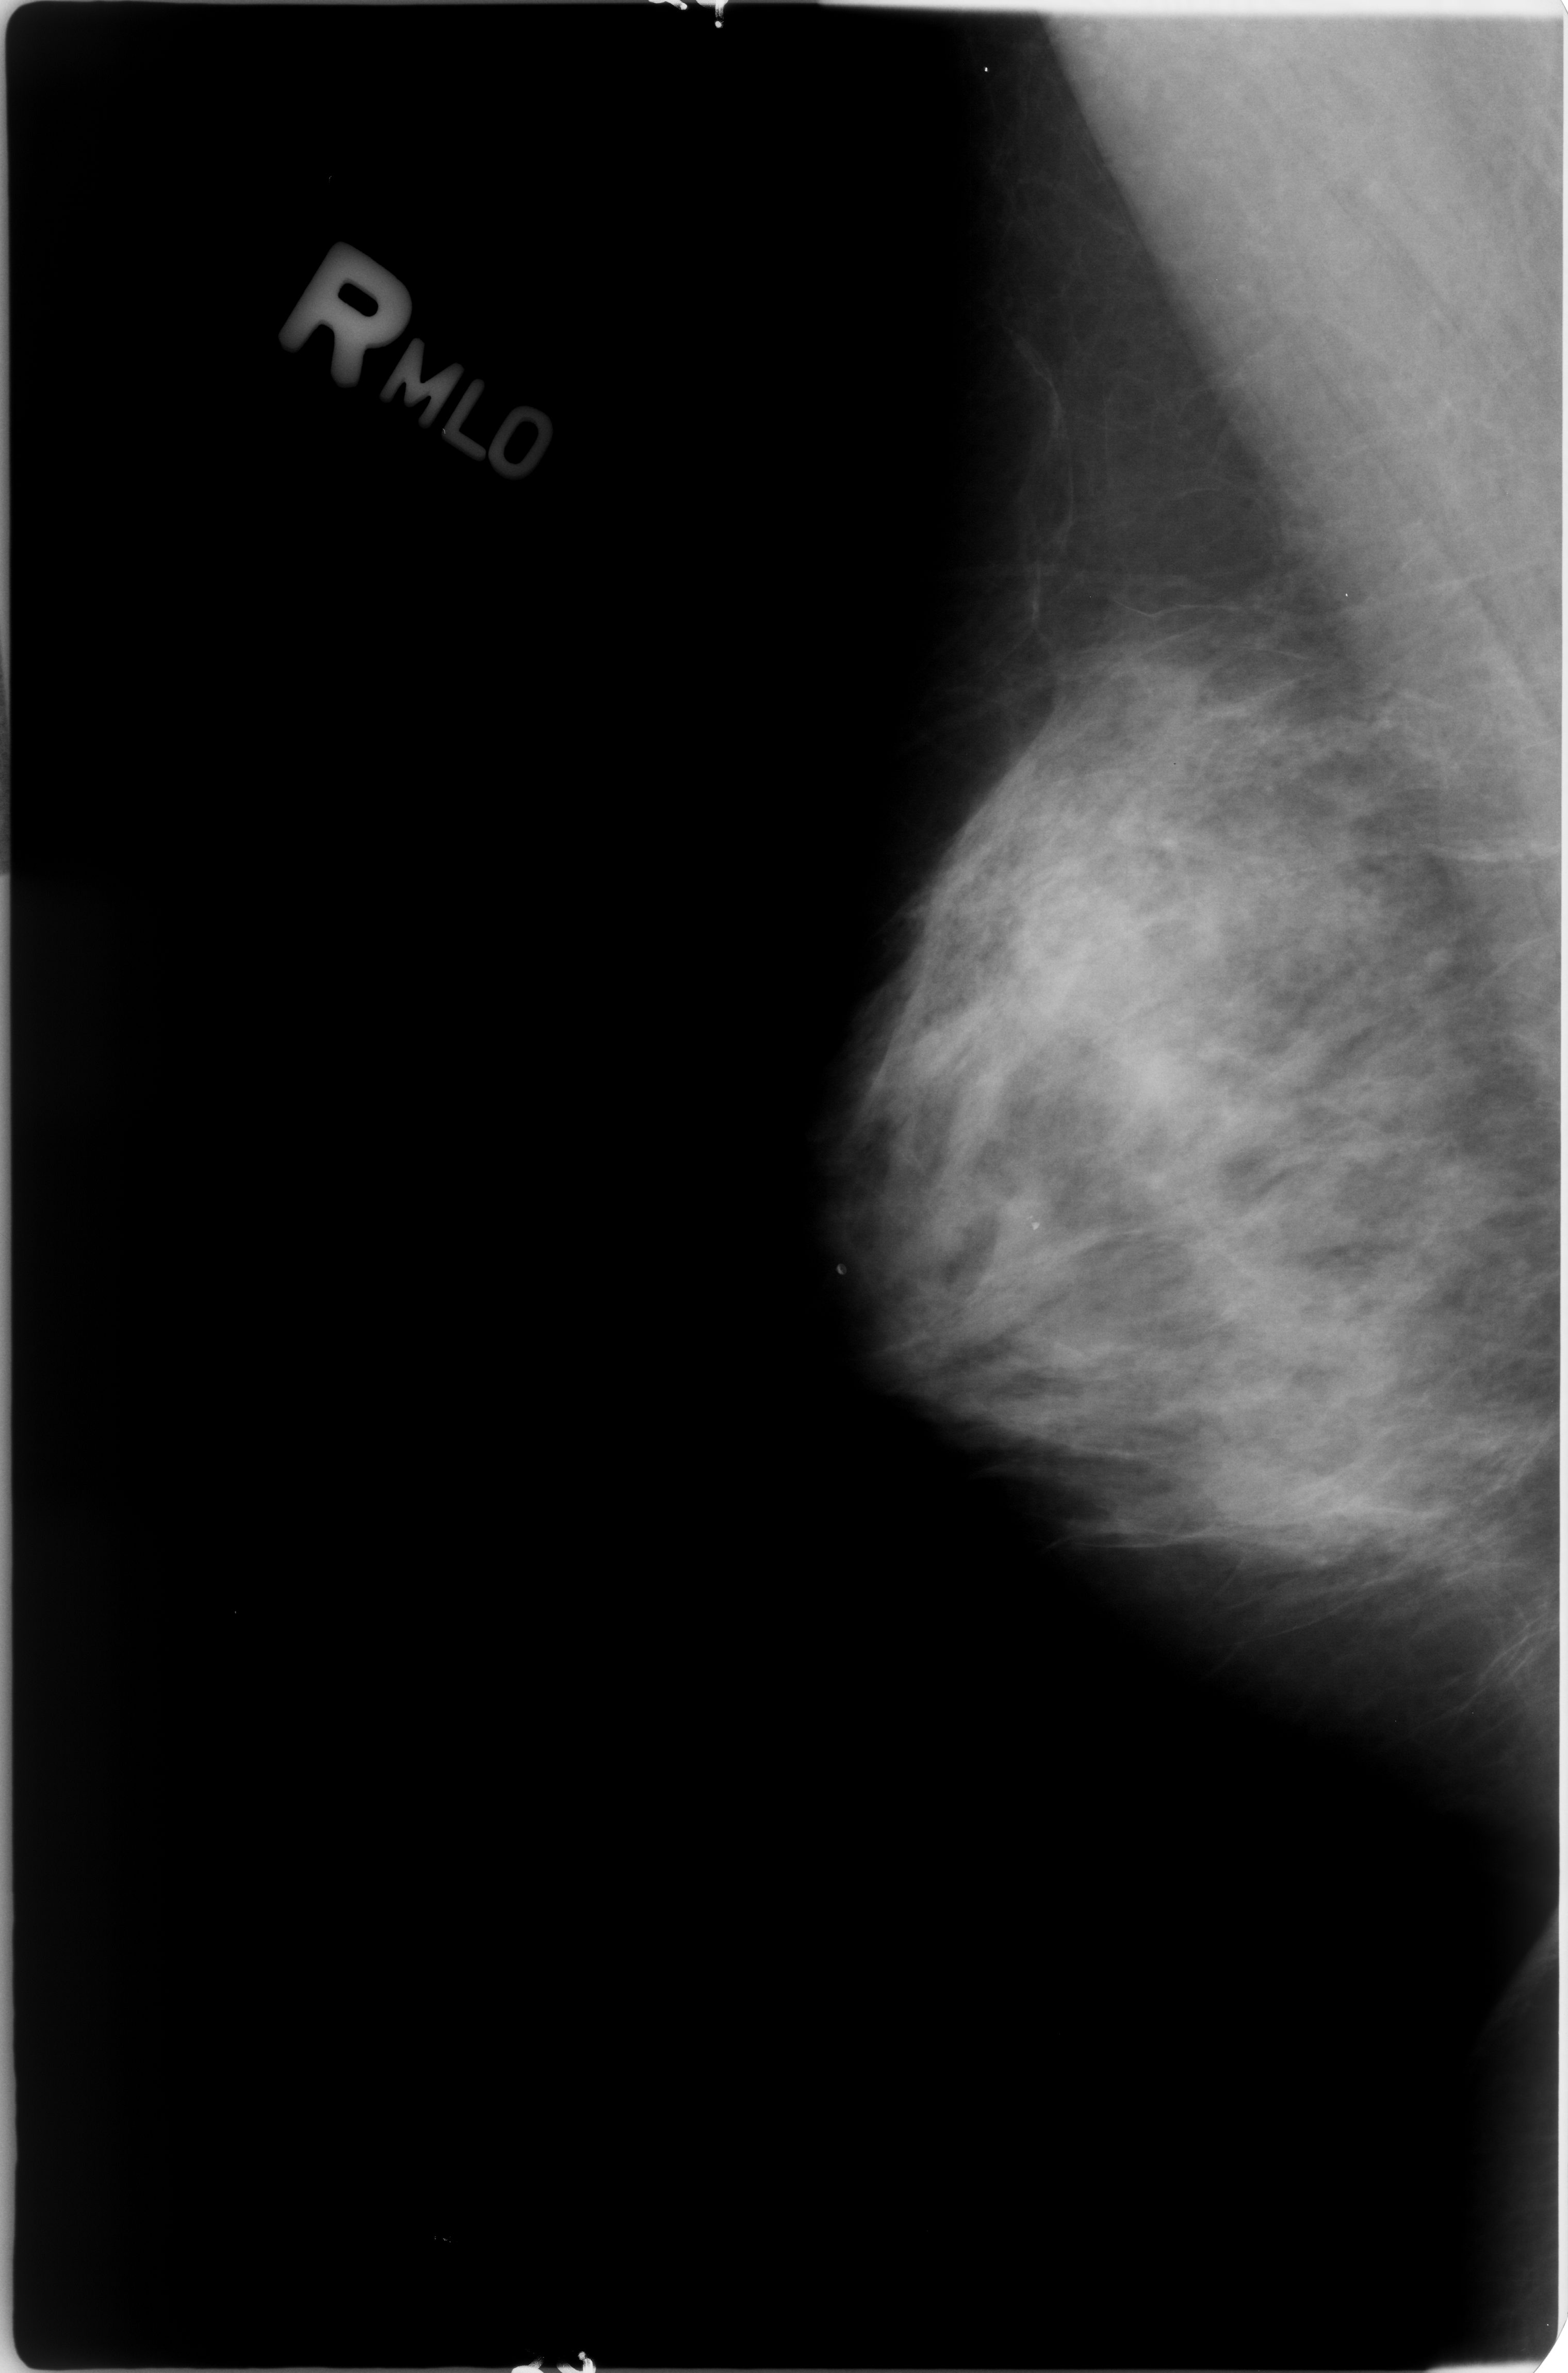
Scanned film-screen mammogram; right breast; MLO view.
- Marked findings (only marked abnormalities are described; nothing is implied about the rest of the image): Finding 1 of 2: calcifications, morphology coarse; BI-RADS assessment category 2; benign; no additional work-up was recommended (benign without callback).
- Finding 2 of 2: calcifications, morphology lucent center; BI-RADS assessment category 2; subtlety rating 3 on a 1 (subtle) to 5 (obvious) scale; benign without callback (not worked up further).